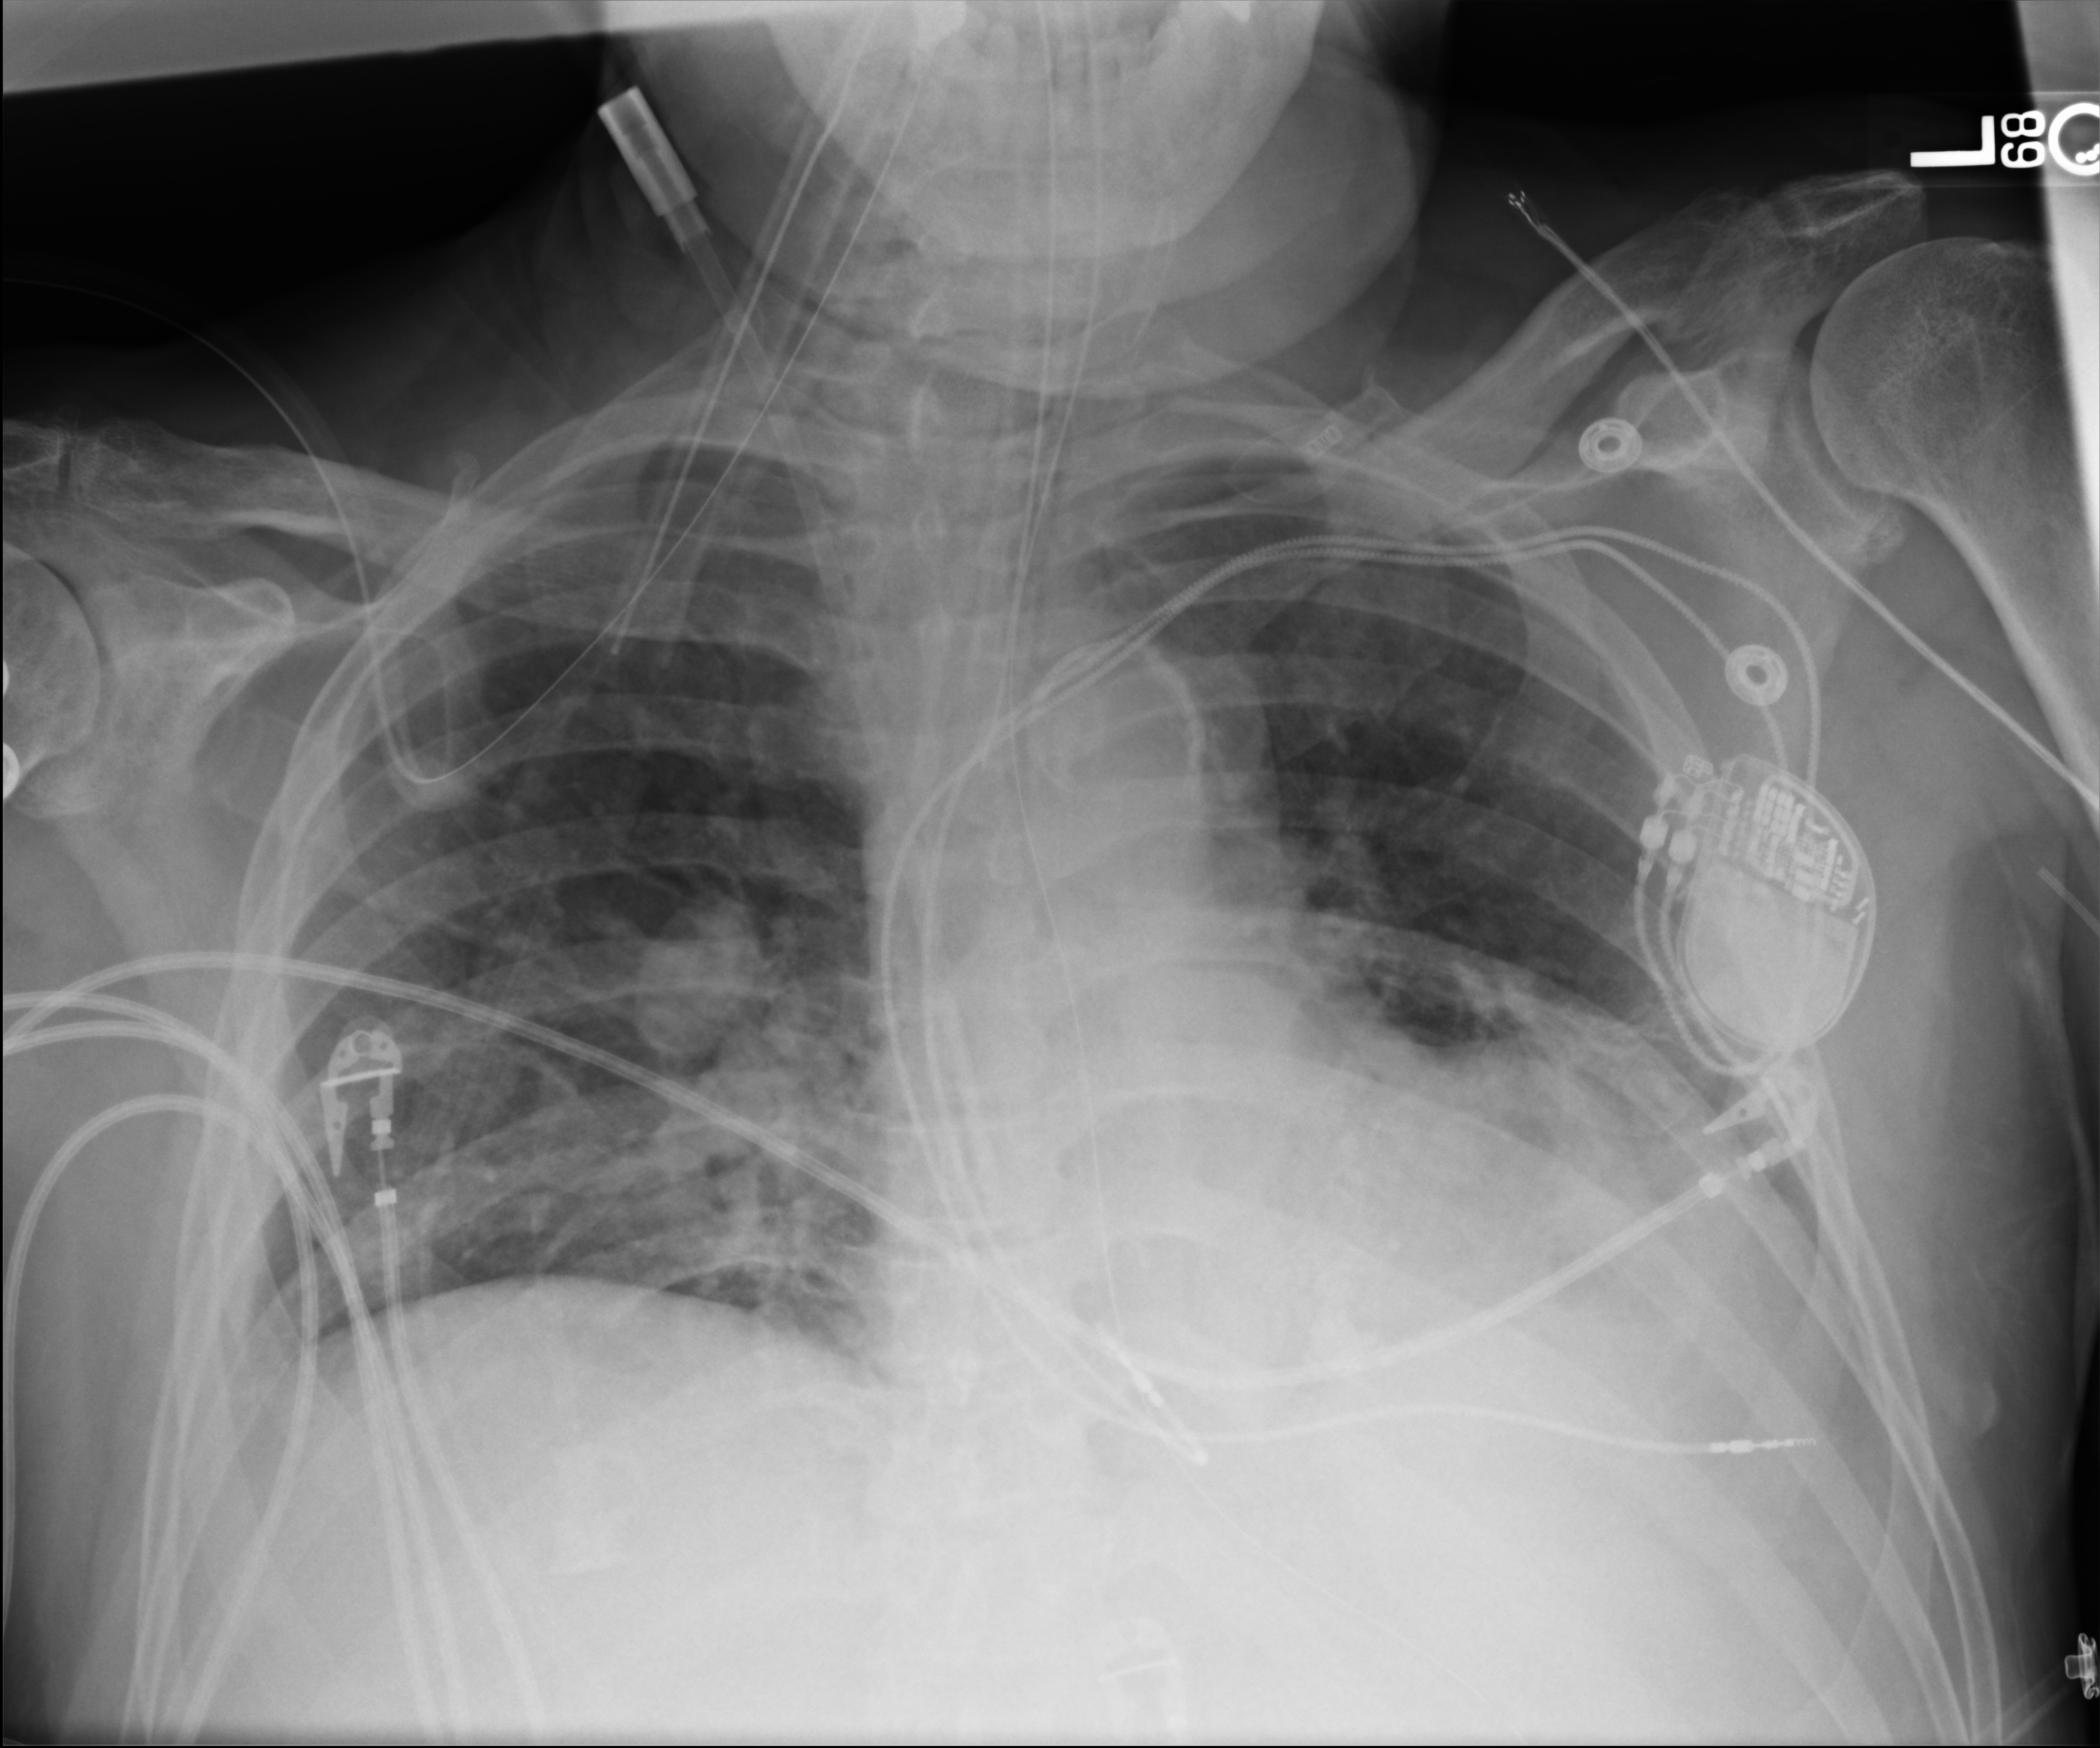
Portable chest radiograph; anteroposterior (AP) projection. Male patient hospitalised with COVID-19, age 60–74 years.
Hospital-stay facts (about this admission, not read from this image; timing relative to this image not recorded):
- length of hospital stay: 41 days
- admitted to intensive care during this hospital stay: yes